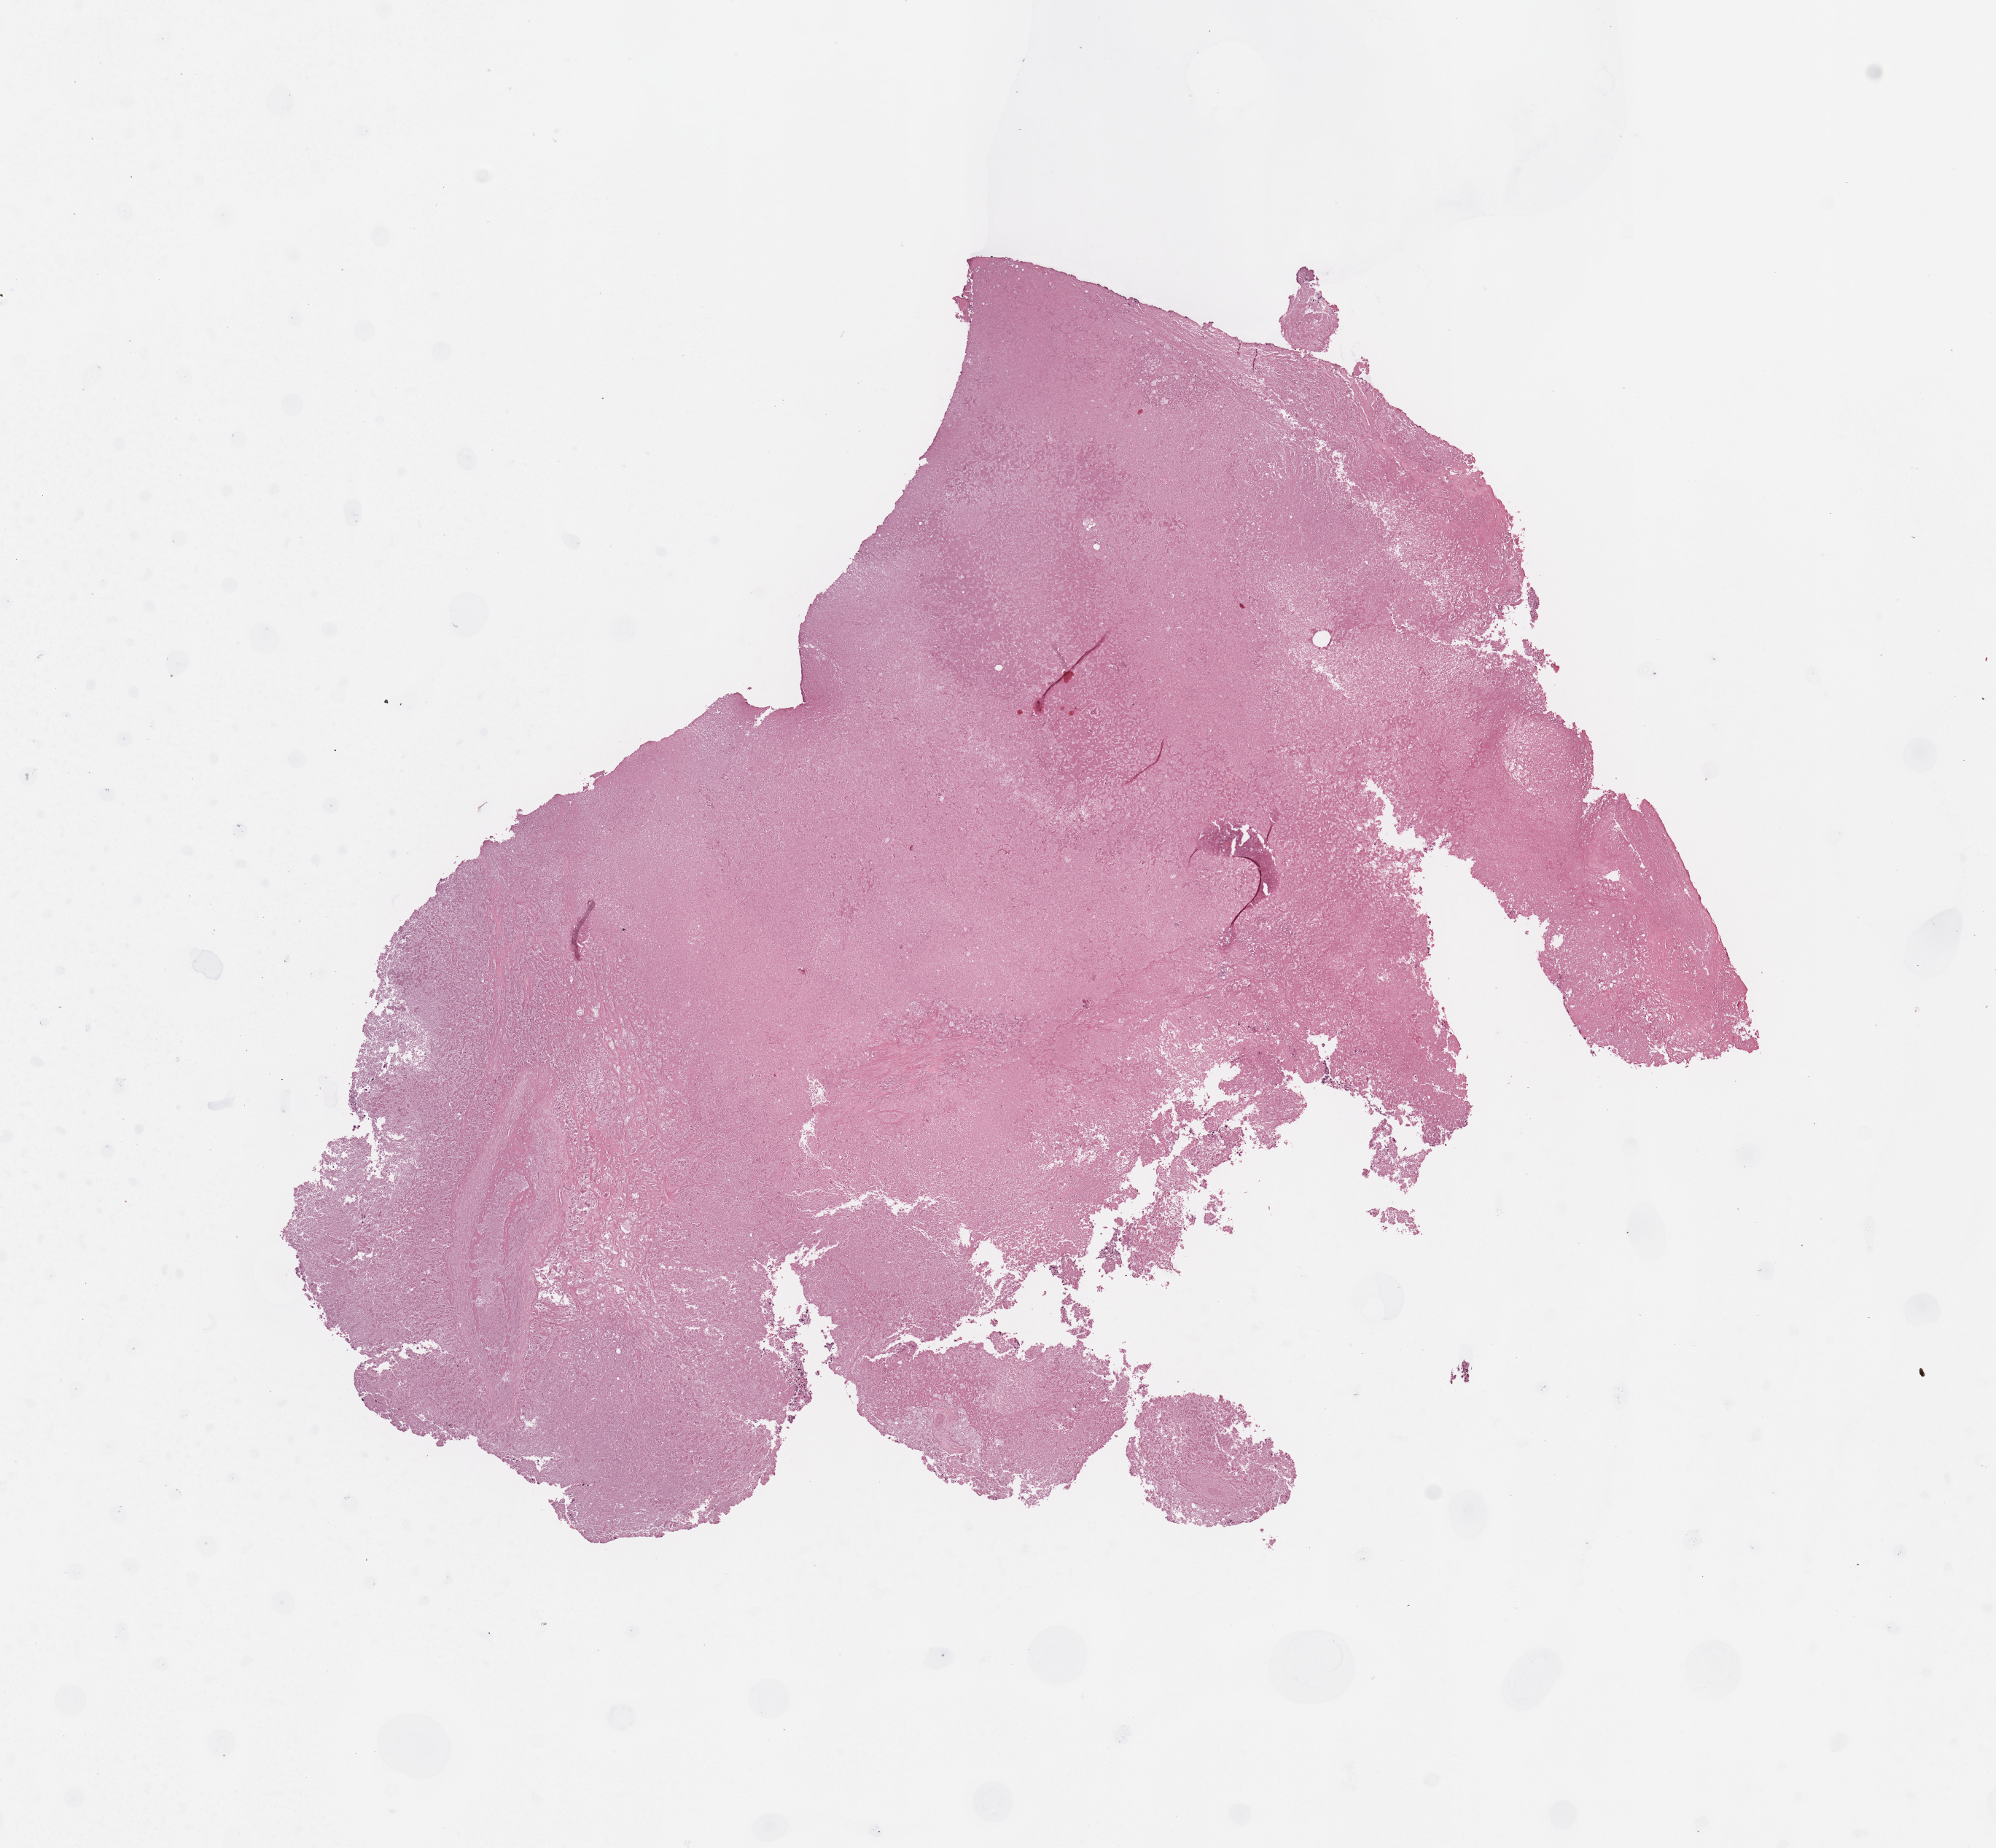
H&E whole-slide image — shown as a low-resolution overview of the whole scanned area (about 10.8 x 10.0 mm). Kidney, tumour tissue. 53-year-old male patient. Histologic grade: G3 (poorly differentiated).
Diagnosis: Renal cell carcinoma, NOS. Primary tumour site (as recorded): middle. AJCC pathologic stage: II.